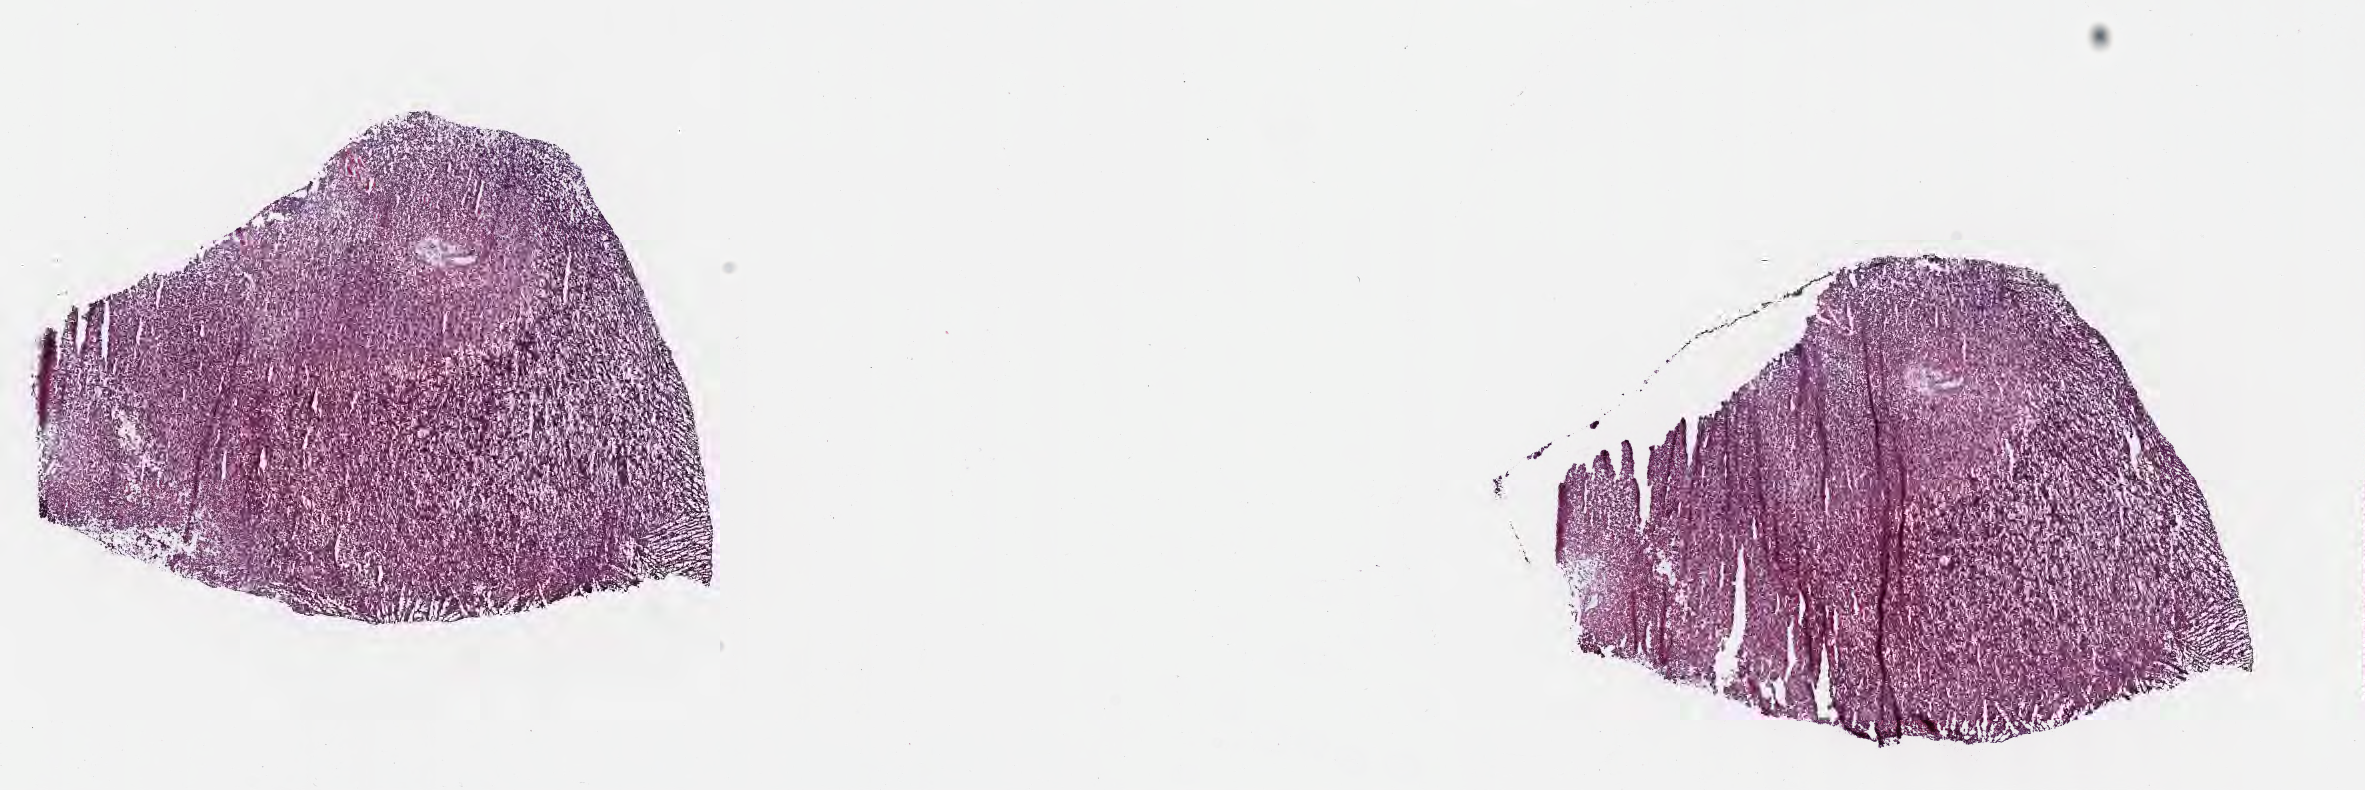
Digitized hematoxylin and eosin (H&E)-stained section, whole scanned area (about 19.1 x 6.4 mm) shown as a low-resolution overview. Frozen section (tissue freezing medium). Primary tumor. Site: mouth. Male, age 9 years at initial diagnosis.
Histologic diagnosis: Burkitt lymphoma, NOS.